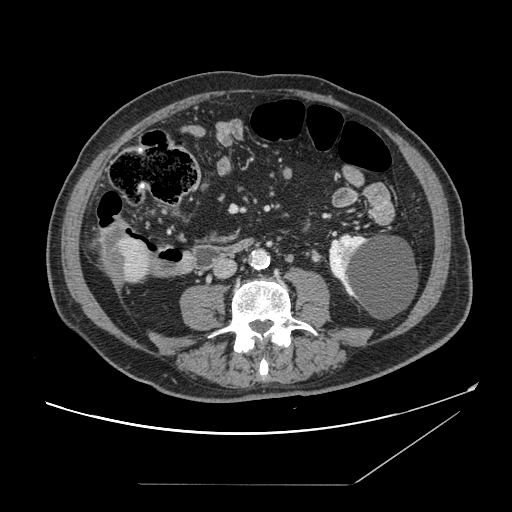
Contrast-enhanced abdominal CT, one axial slice. Position 26 of 166 along the scan axis. 120 kVp. Intravenous contrast given. Soft-tissue window (W 400 / L 40 HU). 2.5 mm slice thickness. 512 × 512 image matrix. Male patient, age 80 years. From the clinical record (not read from this slice): diagnosis: colorectal cancer liver metastases, imaged before liver resection; multiple liver metastases: no; largest metastasis: 2.2 cm; disease in both lobes: no.
Annotated regions visible in this slice (manually delineated by an expert):
- liver: bounding box (x1, y1, x2, y2) in pixels: (99, 229, 152, 286)
- liver metastasis: (104, 230, 128, 283)